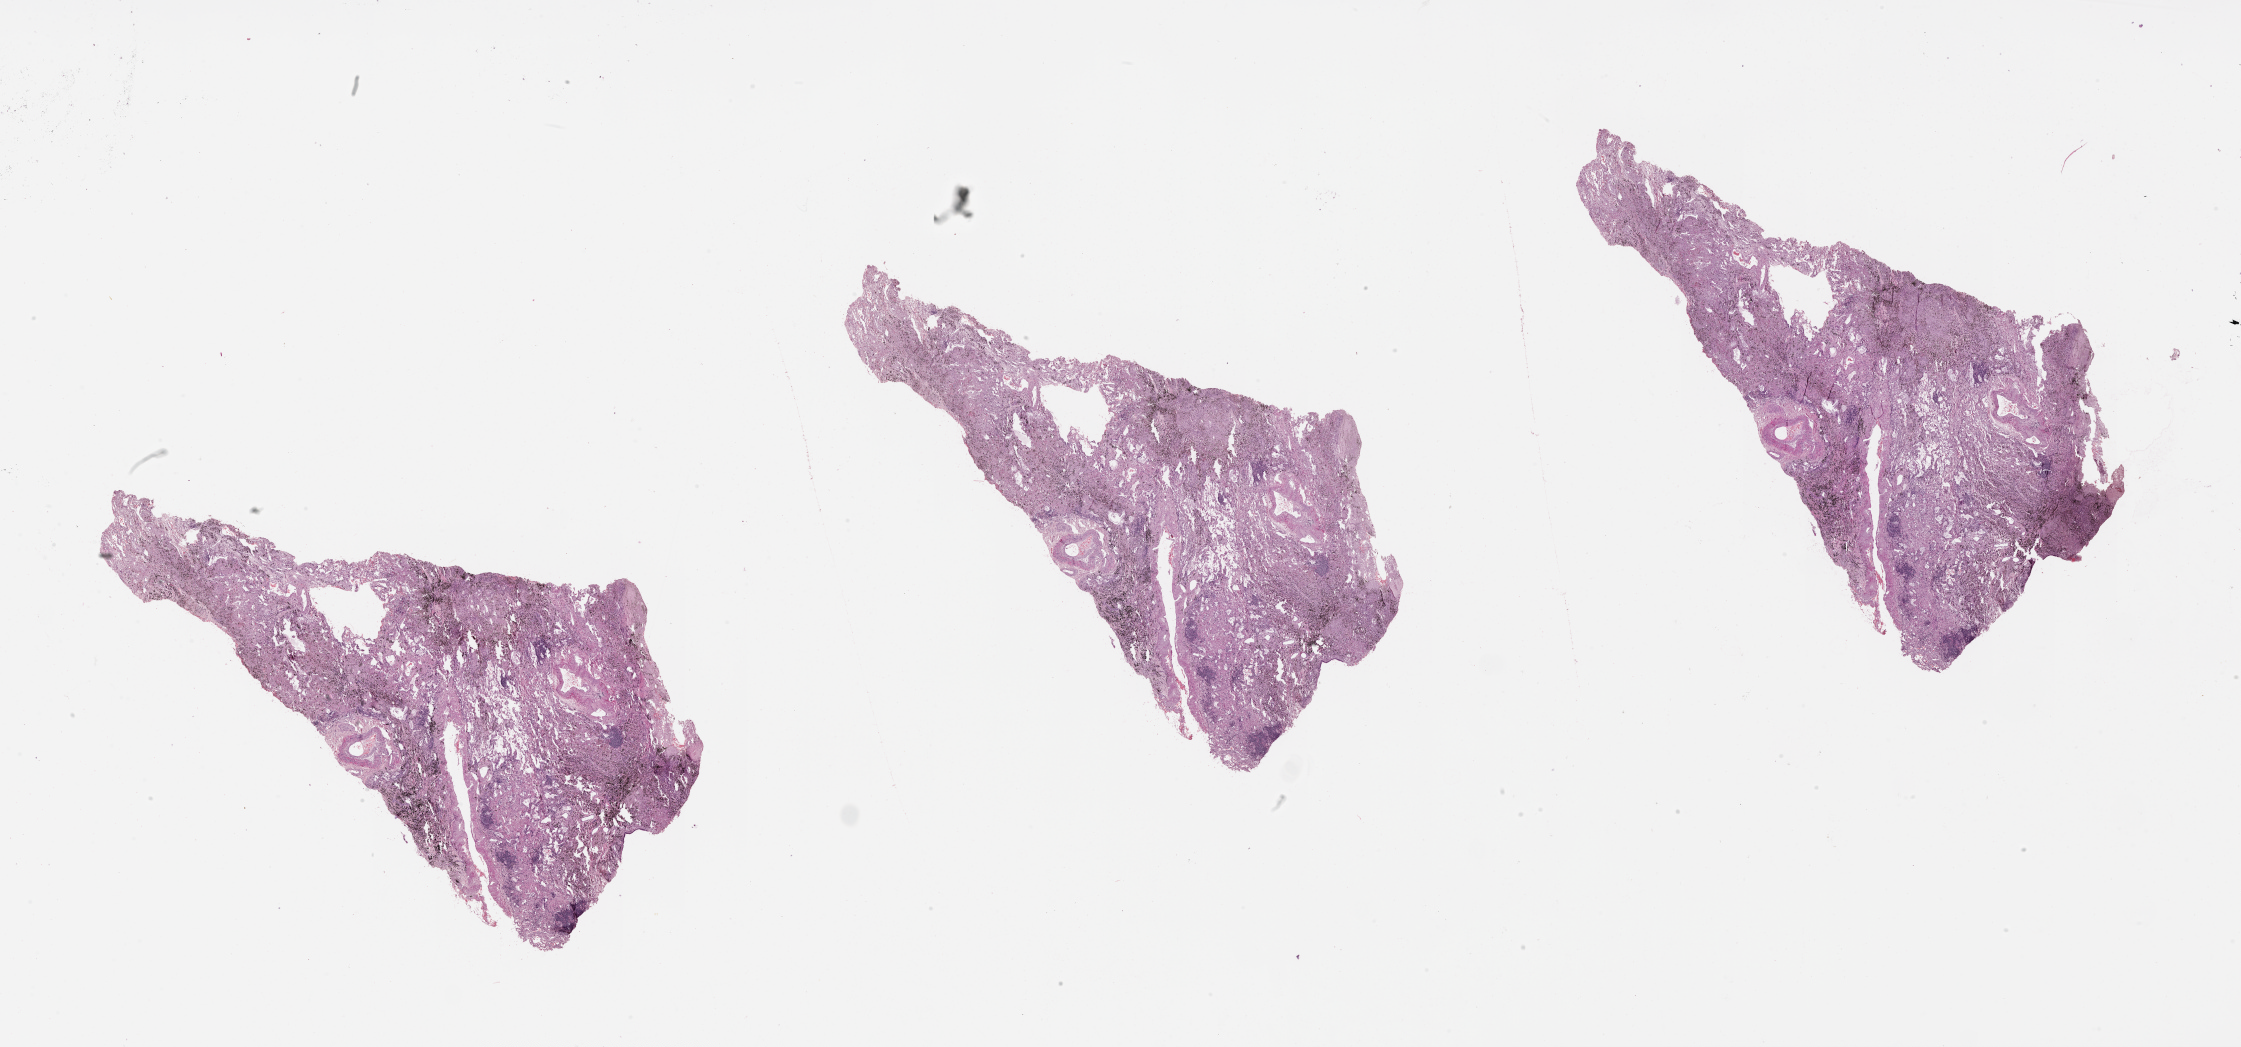
Hematoxylin and eosin (H&E) stained whole-slide image, whole scanned area (about 36.1 x 16.9 mm, acquisition: 20x scan) shown as a low-resolution overview. Normal (non-tumour) tissue sample, lung. Male, 68 y/o.
This section: normal (non-tumour) tissue from the same patient. Patient diagnosis (cohort enrolment): squamous cell carcinoma (lung).